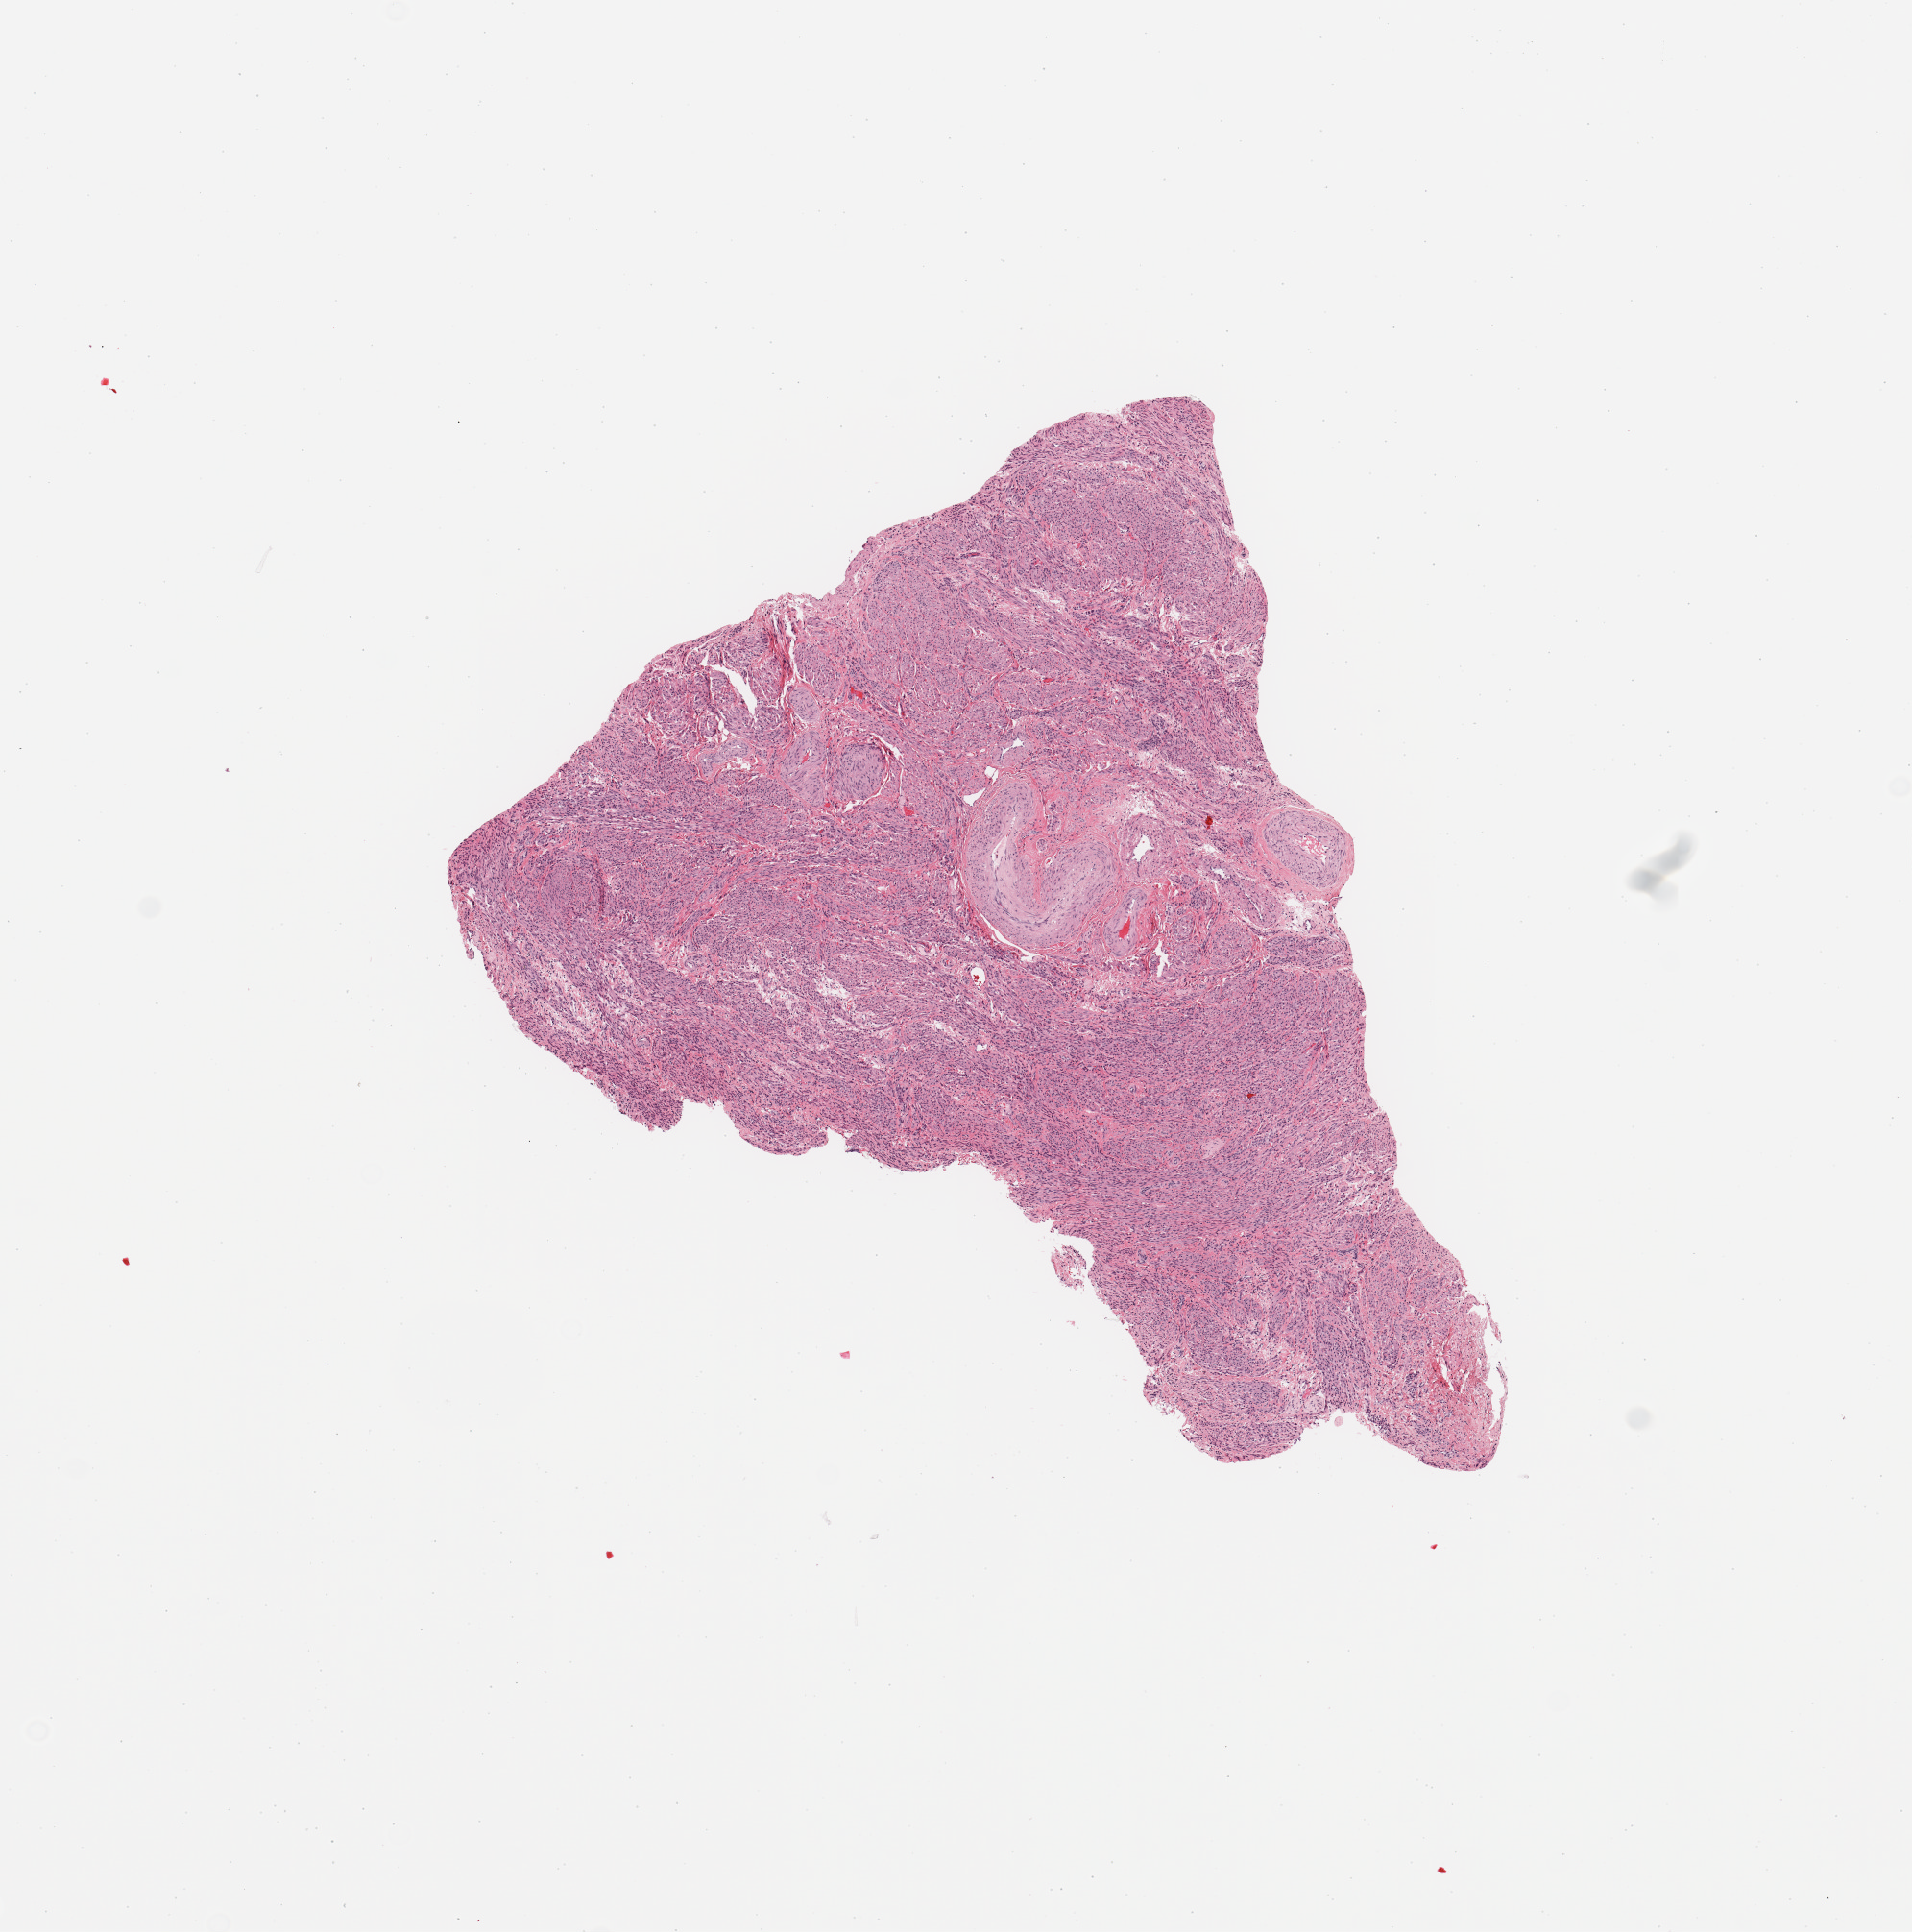
Hematoxylin and eosin (H&E) stained whole-slide image — shown as a low-resolution overview of the whole scanned area (about 7.9 x 8.0 mm, slide scanned at 20x), uterus, normal (non-tumour) tissue. 71-year-old female patient.
This section: normal (non-tumour) tissue from the same patient. Patient diagnosis: Endometrioid adenocarcinoma, NOS.